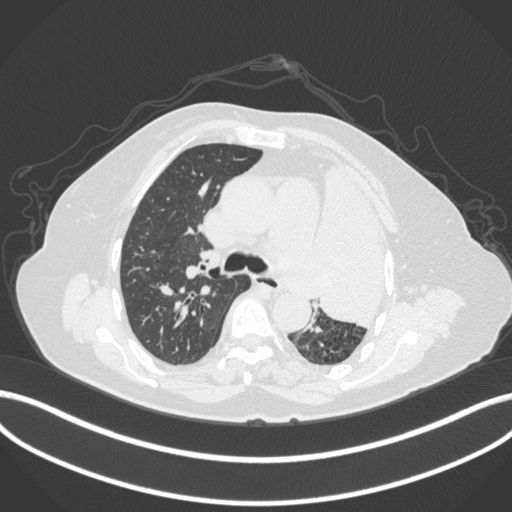
Chest CT, one axial slice; position 254 of 399 along the scan axis; reconstruction kernel B31f; 120 kVp; lung window (W 1500 / L -600 HU); 1 mm slice thickness; 512 × 512 image matrix, field of view 400 × 400 mm. Female patient, age 75 years. From the clinical record (not read from this slice): clinical TNM (as recorded): T3 N3 M1.
Outlined on this slice (bounding box drawn by a radiologist):
- lung tumour (recorded histology: adenocarcinoma): bounding box [x1, y1, x2, y2] px = [315, 157, 403, 331]